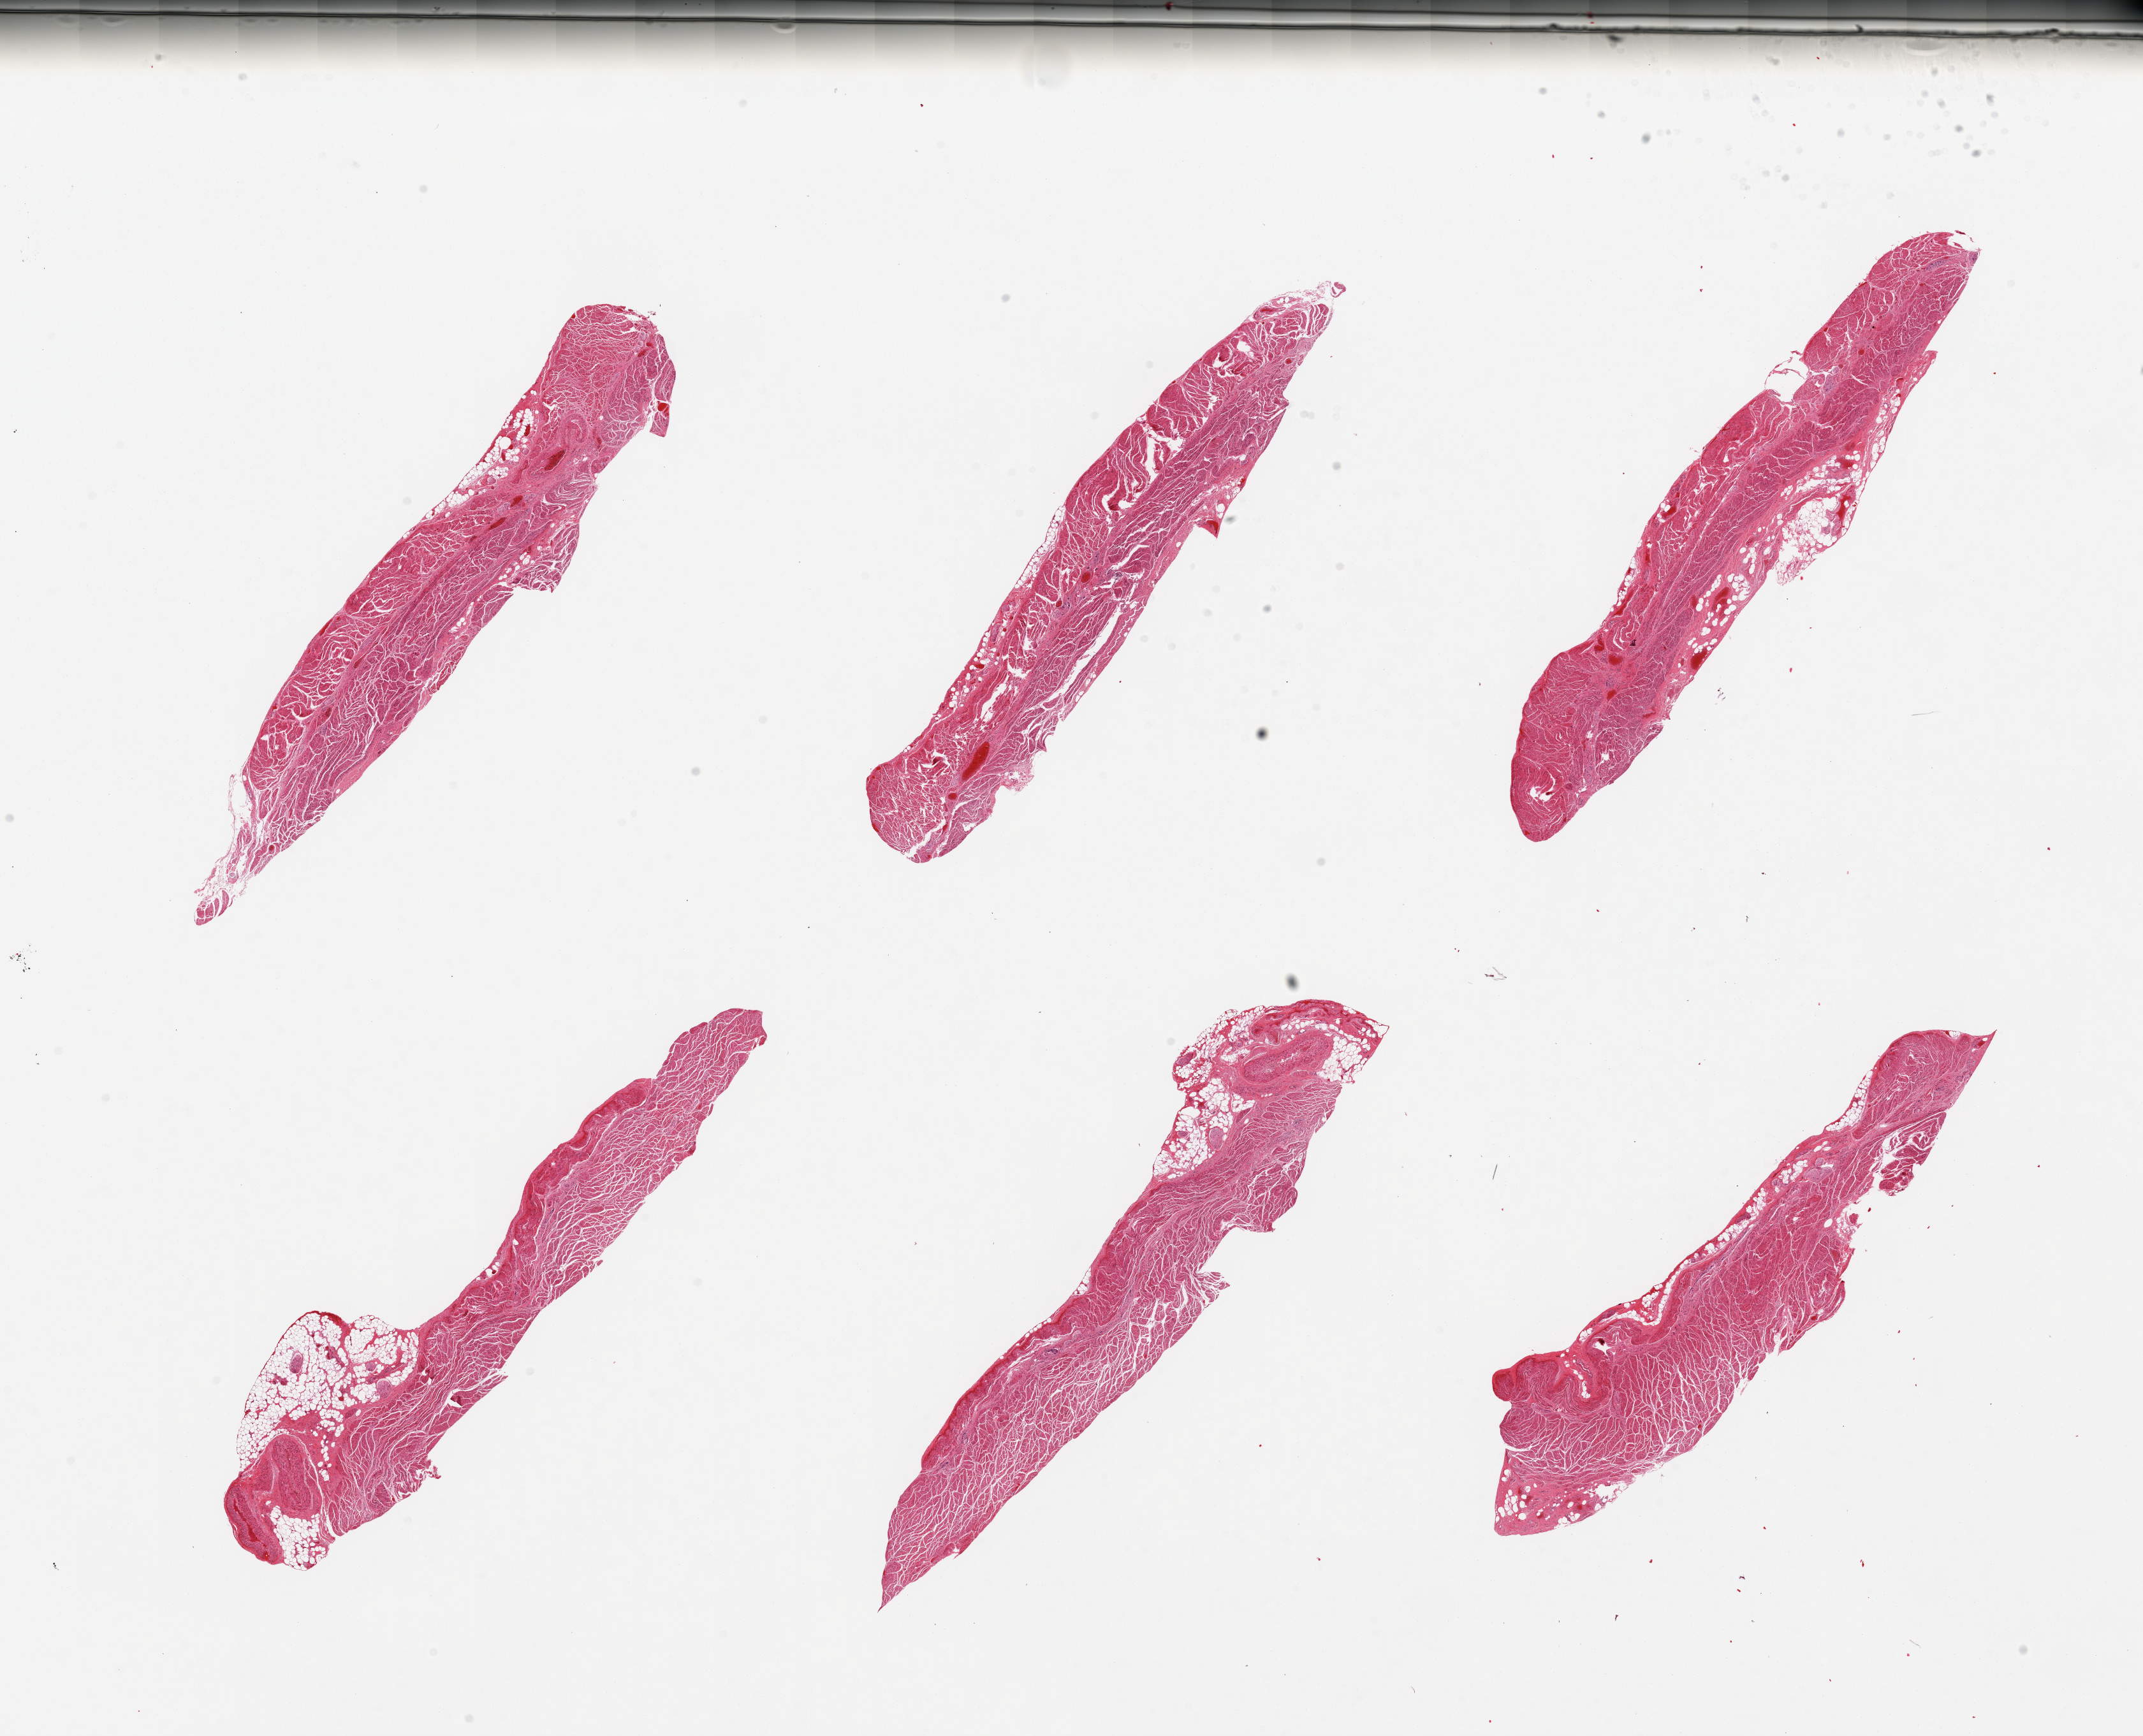
Whole-slide image, hematoxylin and eosin (H&E) stain, low-resolution overview of the scanned area, about 26.6 x 21.5 mm. PAXgene-fixed, paraffin-embedded tissue. Target tissue: gastroesophageal junction. Donor tissue sample. Donor sex: male.
Pathologist's review note for this sample: 6 pieces; muscularis, few pieces with attached fat, larger vessels, and nerve.